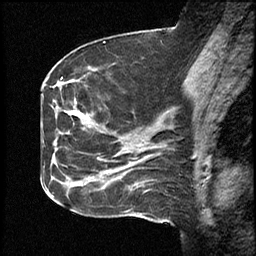
Breast MRI (dynamic contrast-enhanced), one sagittal slice; slice 22 of 46 in the series (ordered by position); dynamic contrast-enhanced study with each time point stored as its own series, time point 2 of 4 at this slice position (early post-contrast, ordered by acquisition time); 1.5 T; TE 4.2 ms, TR 18.3 ms; 256 × 256 image matrix. Case-level facts recorded for this patient, not image findings: setting: breast cancer imaged before/during neoadjuvant chemotherapy; receptor status: HR-positive, HER2-negative.
Annotated regions visible in this slice (semi-automatically segmented with operator editing):
- analysis volume of interest (the breast-tissue region the enhancement analysis was run in; not a lesion): box from (x=64, y=71) to (x=111, y=200) px
- tumour enhancement mask (voxels above the 100 % enhancement threshold inside the analysis volume of interest): (x=73, y=111)–(x=79, y=115)